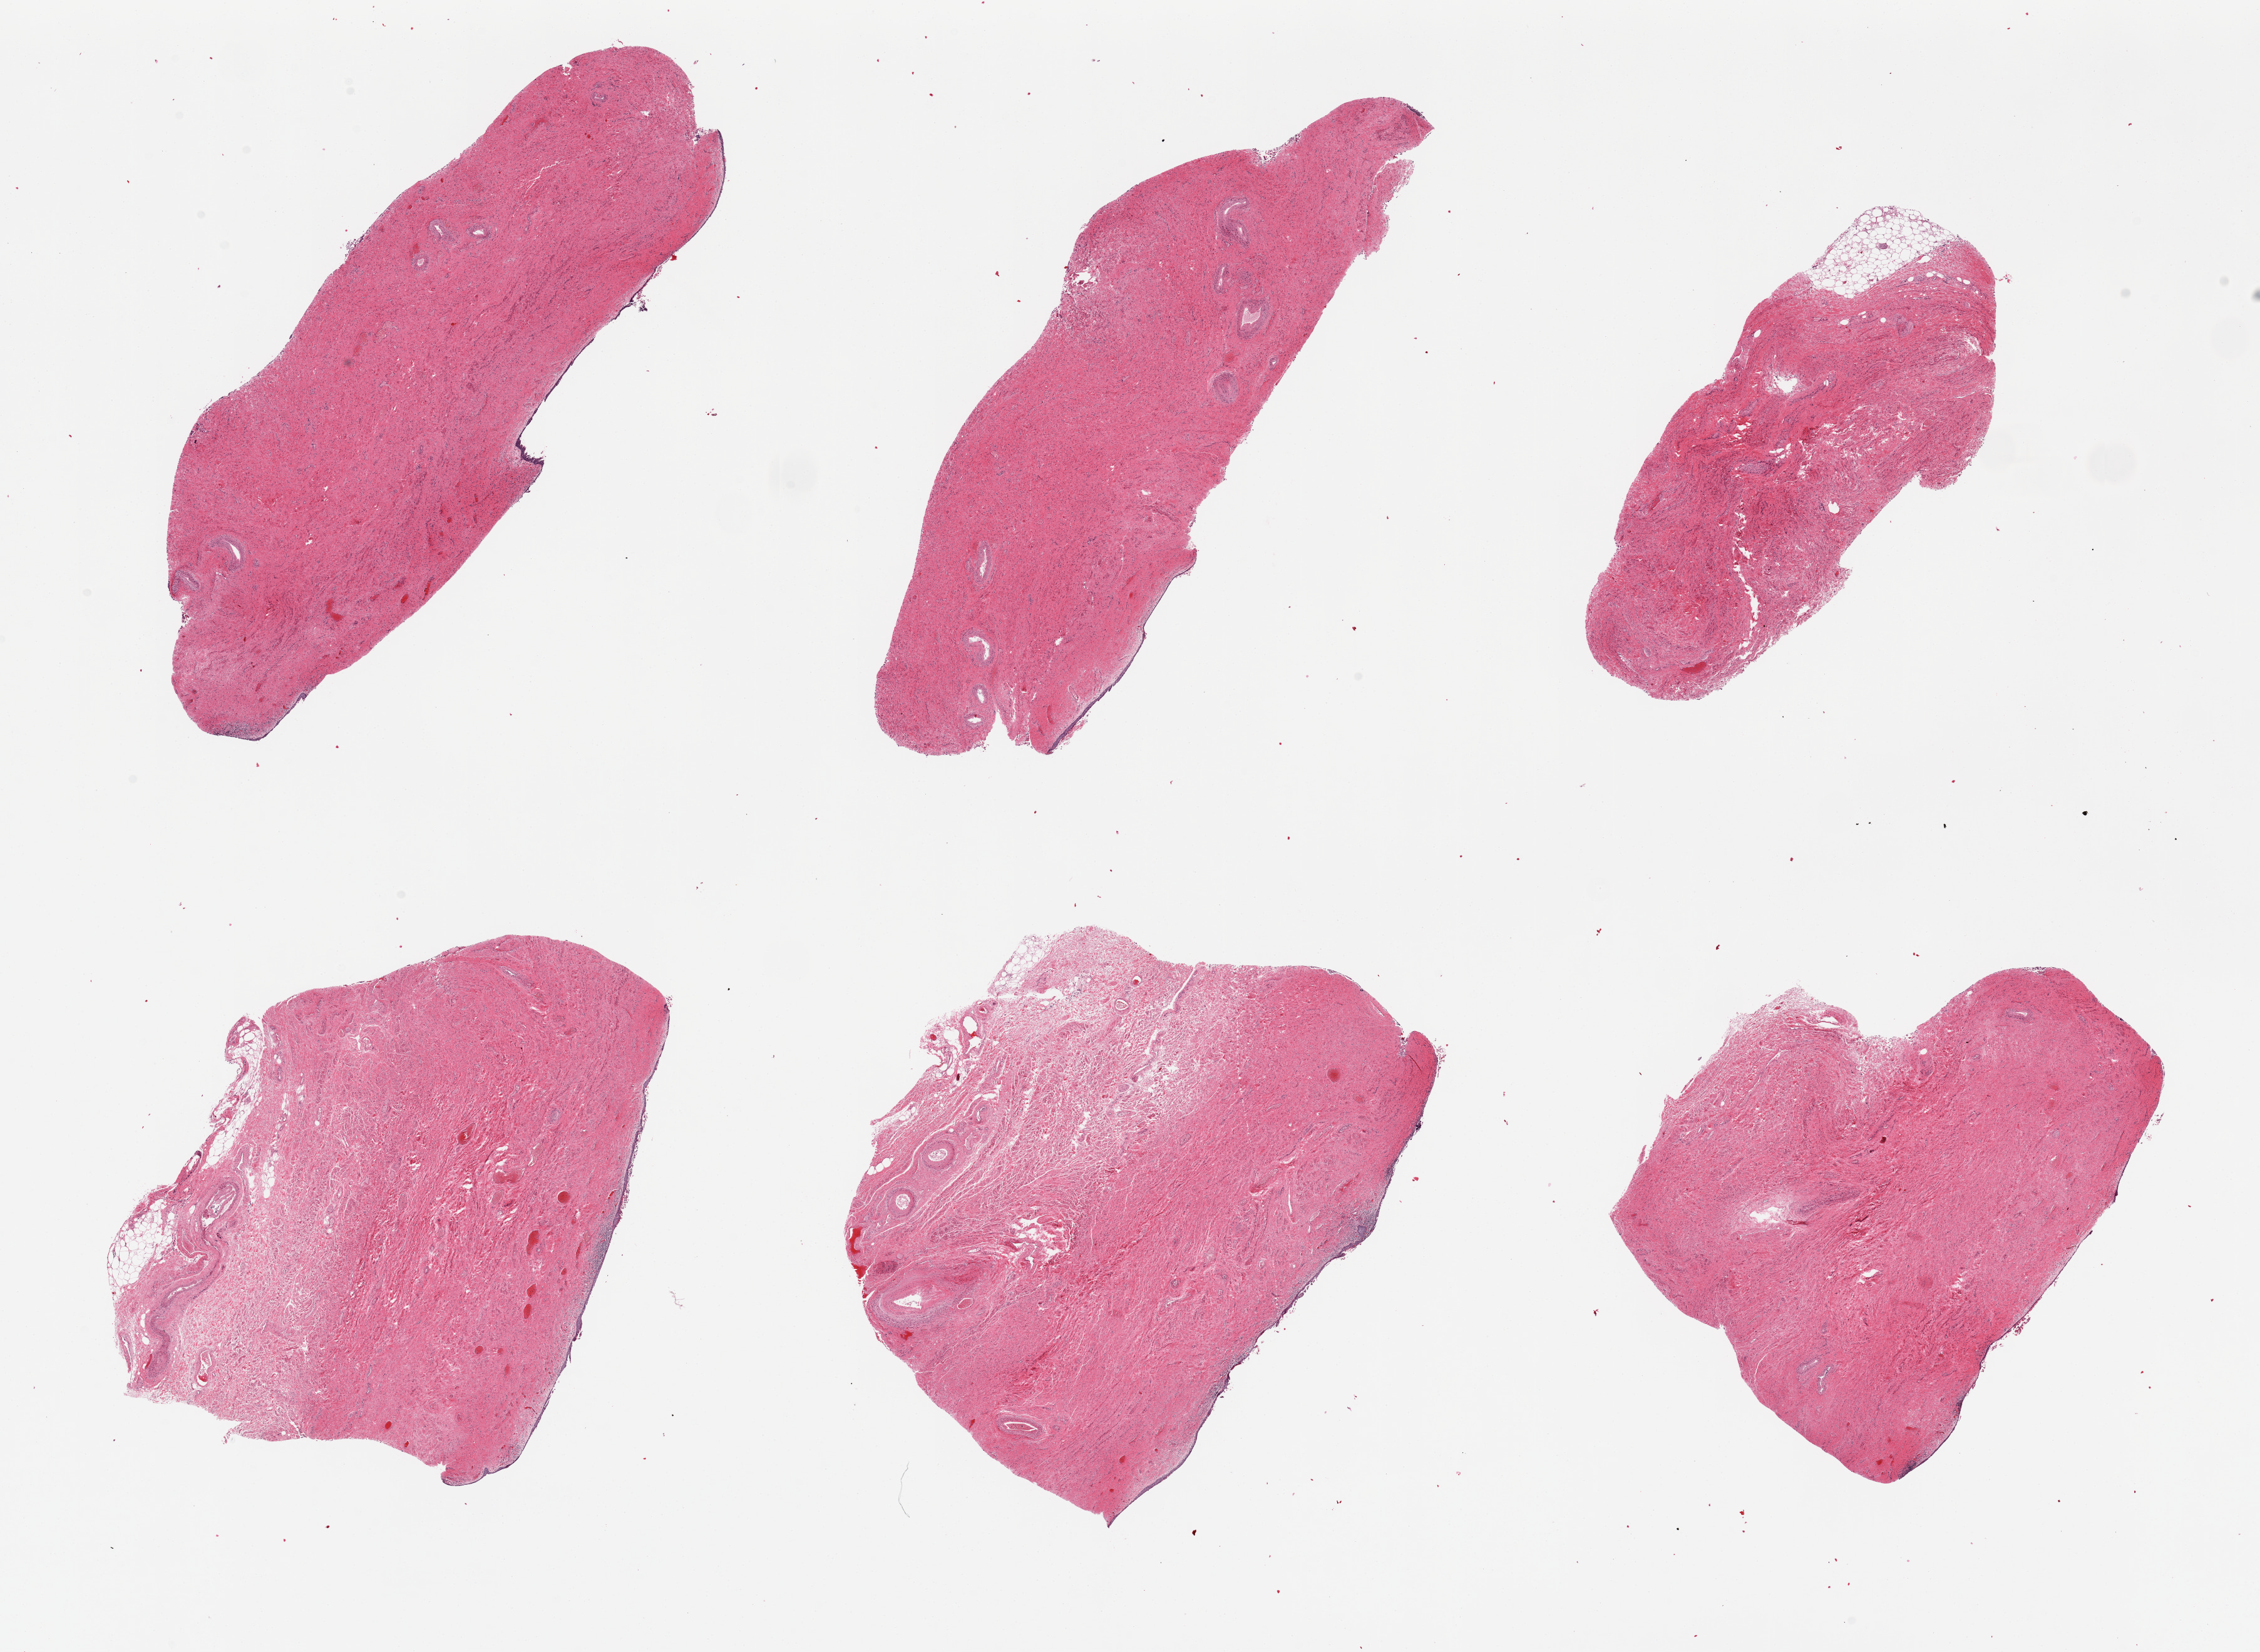
Digitized H&E-stained section, brightfield — low-resolution overview of the scanned area, about 28.5 x 20.9 mm (acquisition: 20x scan); PAXgene-fixed, paraffin-embedded tissue; sampled site (target tissue): vagina; donor tissue sample. Donor sex: female.
Reviewer comment on this tissue sample: 6 pieces, mucosa mostly sloughed.